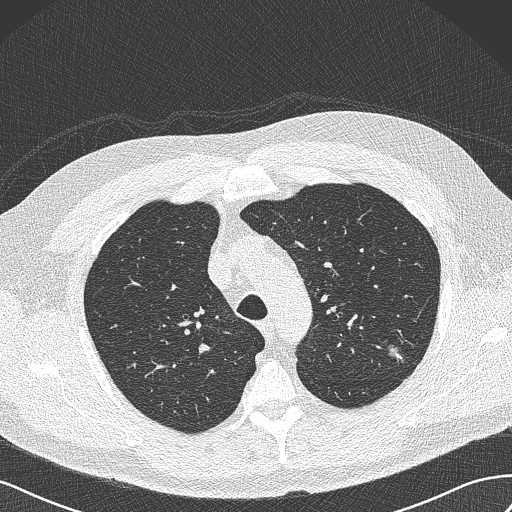
Axial slice from a low-dose chest CT screening exam; first (baseline) screen; lung window (W 1500 / L -600 HU); 1 mm slice thickness; 512 × 512 image matrix, field of view 360 × 360 mm. Male, age 65 years at enrolment. Former smoker at enrolment.
Lesion marked by an expert reader, bounding box [x1, y1, x2, y2] px = [383, 341, 417, 372]. The screening reader recorded 3 non-calcified nodules or masses ≥4 mm on this exam (left upper lobe, left upper lobe, right upper lobe); which of them this box marks is not recorded. Official screen result: positive, change unspecified: nodule(s) >= 4 mm or enlarging nodule(s), mass(es), or other non-specific abnormalities suspicious for lung cancer. Lung cancer was diagnosed 541 days after this screen: adenocarcinoma, NOS, left upper lobe, poorly differentiated (G3), stage IA (AJCC 6th edition), 13 mm at pathology.